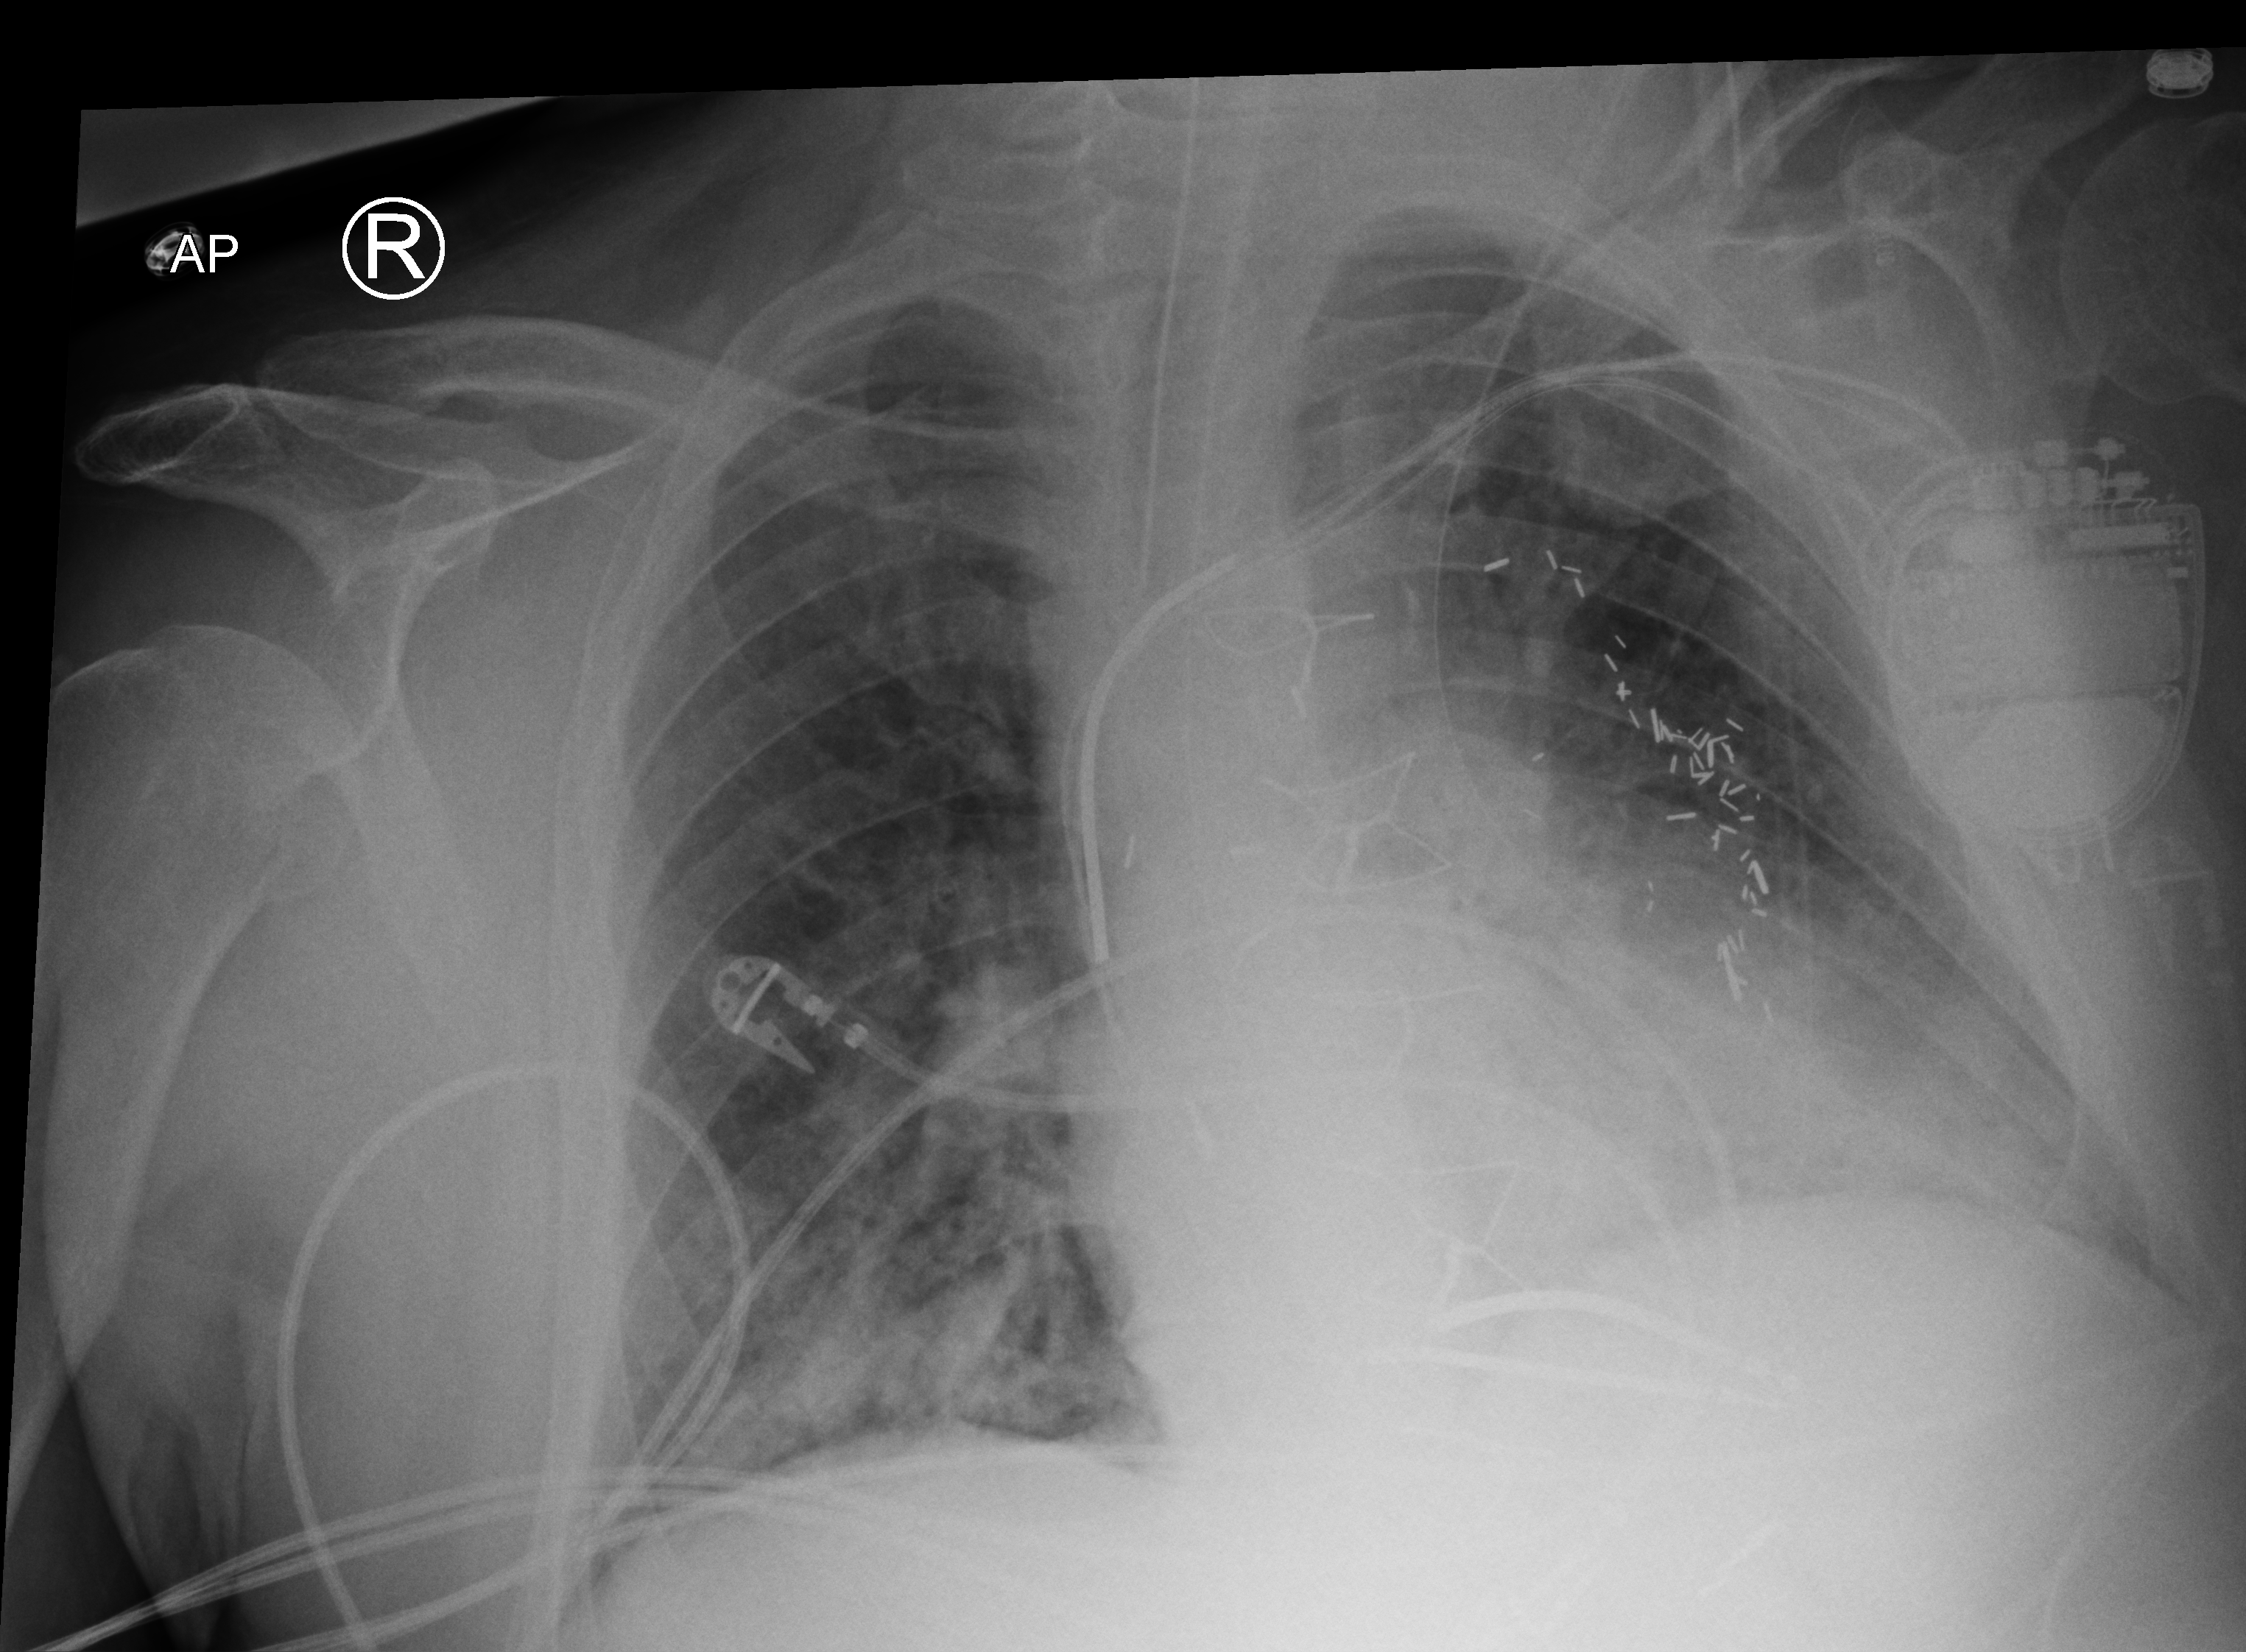
Chest X-ray (portable), anteroposterior (AP) projection. Male patient hospitalised with COVID-19, age 60–74 years.
Admission-level facts for this patient (not findings on this image; timing relative to this image not recorded):
- admitted to intensive care during this hospital stay: yes